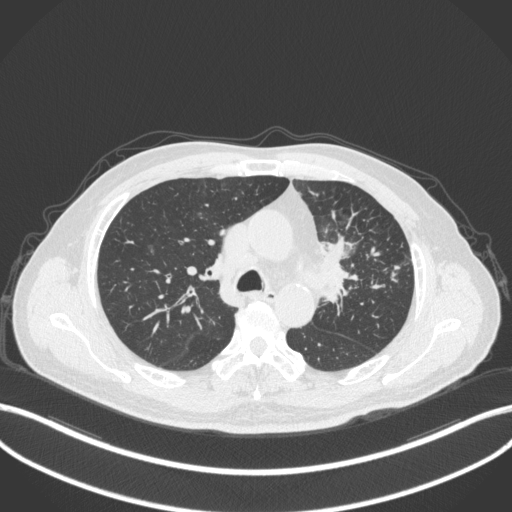
Chest CT, one axial slice. Slice 233 of 386 in the series (ordered by position). Reconstruction kernel B31f. Lung window (W 1500 / L -600 HU). 1 mm slice thickness. 512 × 512 image matrix, field of view 400 × 400 mm. Male patient, age 69 years. Case-level facts recorded for this patient, not image findings: clinical TNM (as recorded): T2a N2 M0.
Outlined on this slice (rectangle marked by the reading radiologist):
- lung tumour (recorded histology: adenocarcinoma): bounding box (x1, y1, x2, y2) in pixels: (317, 231, 358, 308)